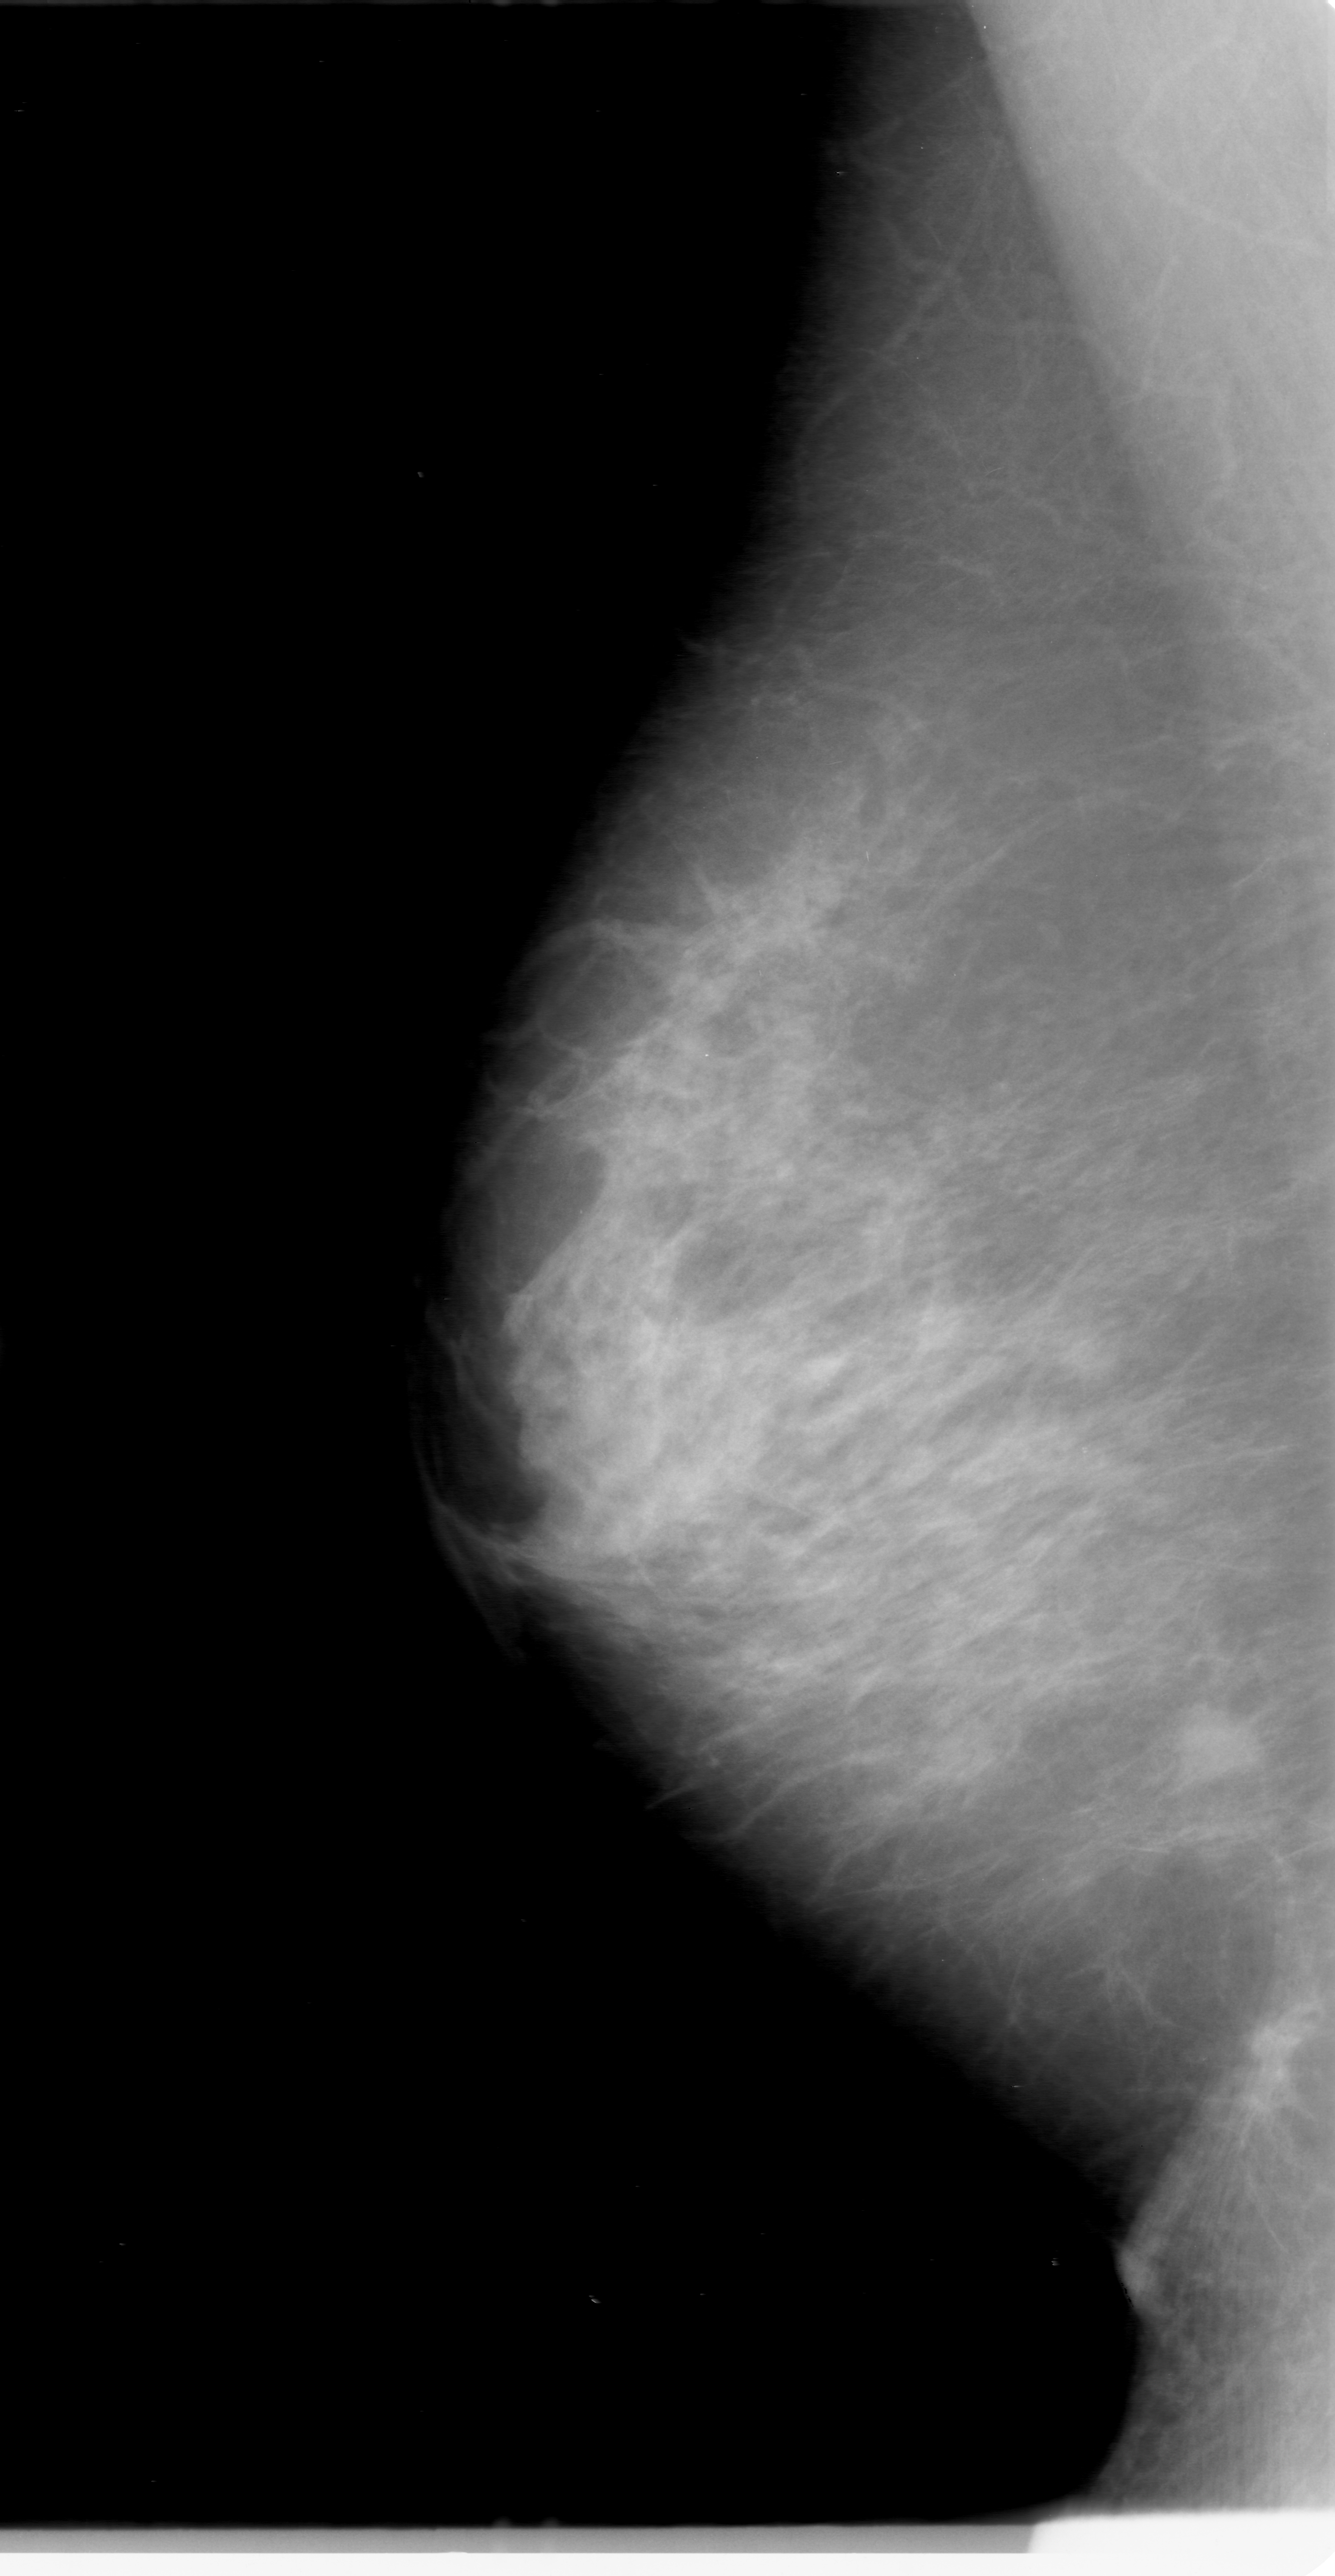
Scanned film-screen mammogram; right breast; MLO view; BI-RADS breast density category 2 (scale 1–4).
Marked findings (only marked abnormalities are described; nothing is implied about the rest of the image): mass, shape oval, margins obscured; BI-RADS assessment category 0; pathology (as recorded): malignant.